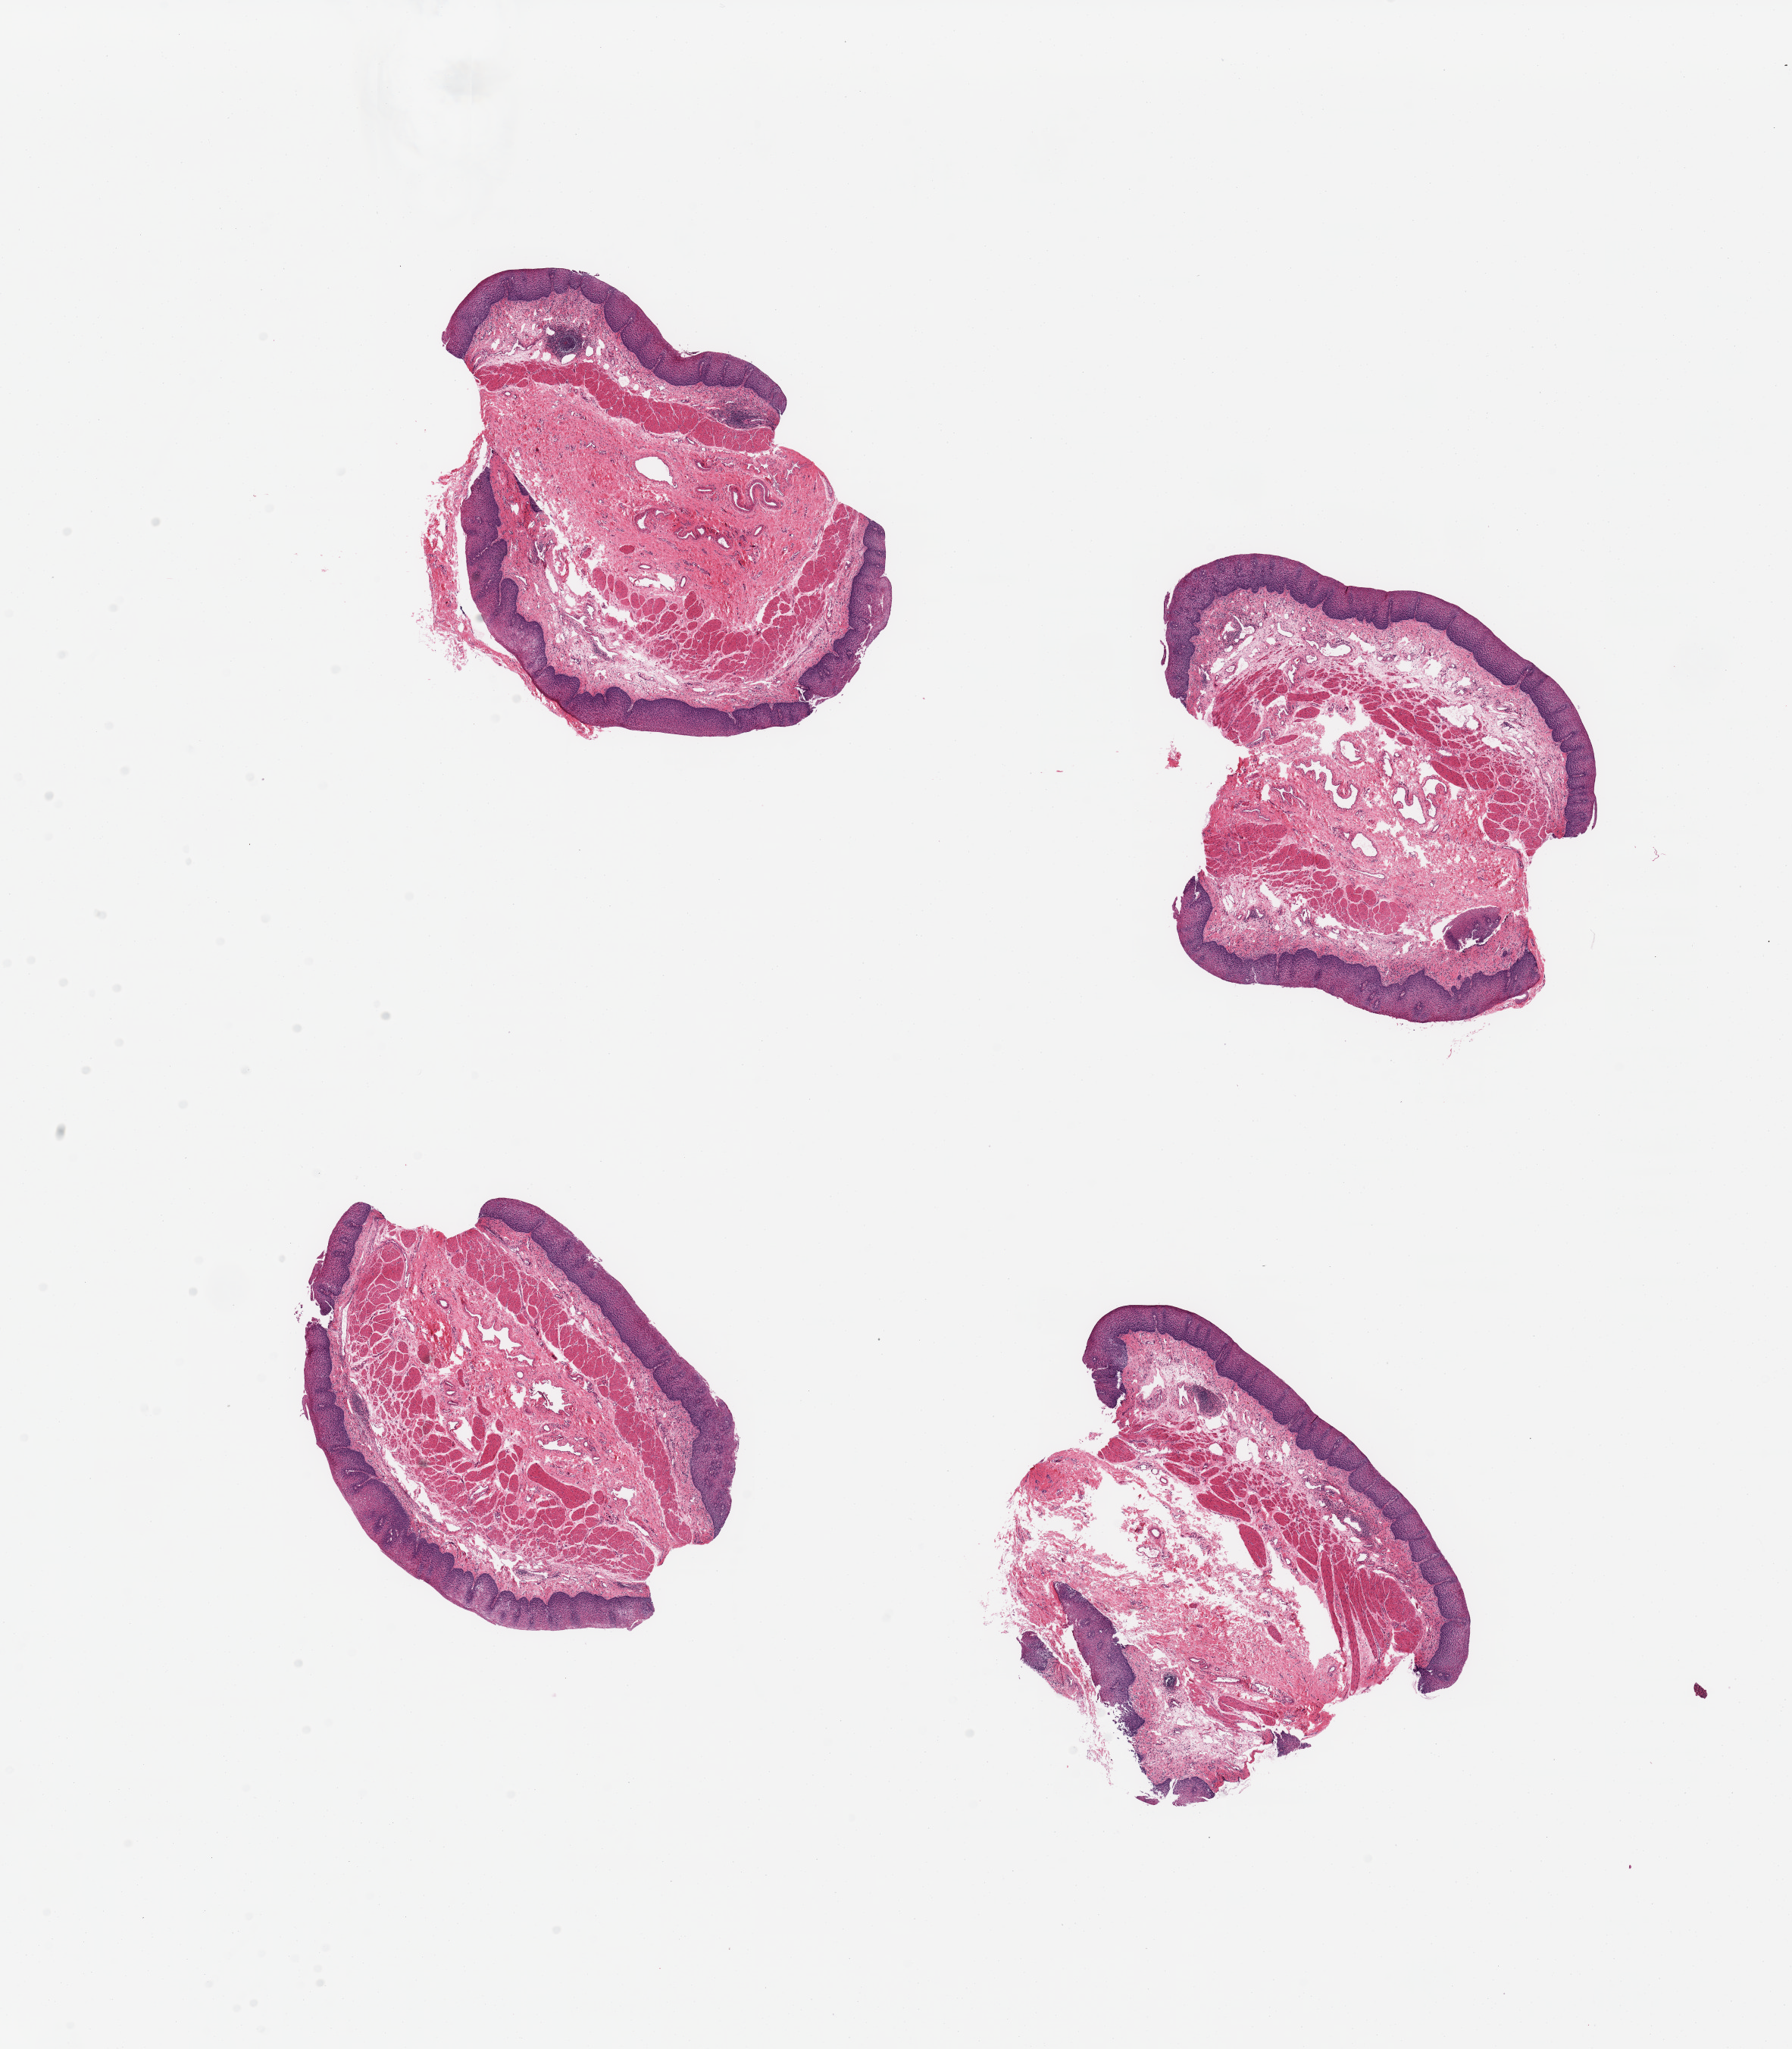
Whole-slide image, H&E stain, shown as a low-resolution overview of the whole scanned area (about 18.7 x 21.4 mm), PAXgene-fixed paraffin-embedded (PFPE) section, sampled site (target tissue): esophageal mucous membrane, donor tissue sample. Donor sex: male.
Review note (as recorded): 4 pieces; ~0.5mm thick stratified squamous epithelium.